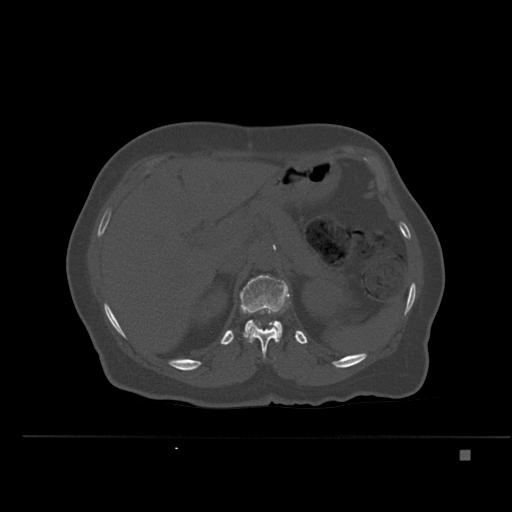
CT including the spine, one axial slice. Position 247 of 477 along the scan axis. Bone window (W 1800 / L 400 HU). 512 × 512 image matrix, field of view 422 × 422 mm. Female patient, age 74 years. From the clinical record (not read from this slice): primary cancer: colon.
Outlined on this slice (semi-automatic segmentation, software-assisted and operator-edited):
- L1 vertebra: box from (x=240, y=275) to (x=290, y=342) px
- T12 vertebra: (x=246, y=302)–(x=290, y=358)